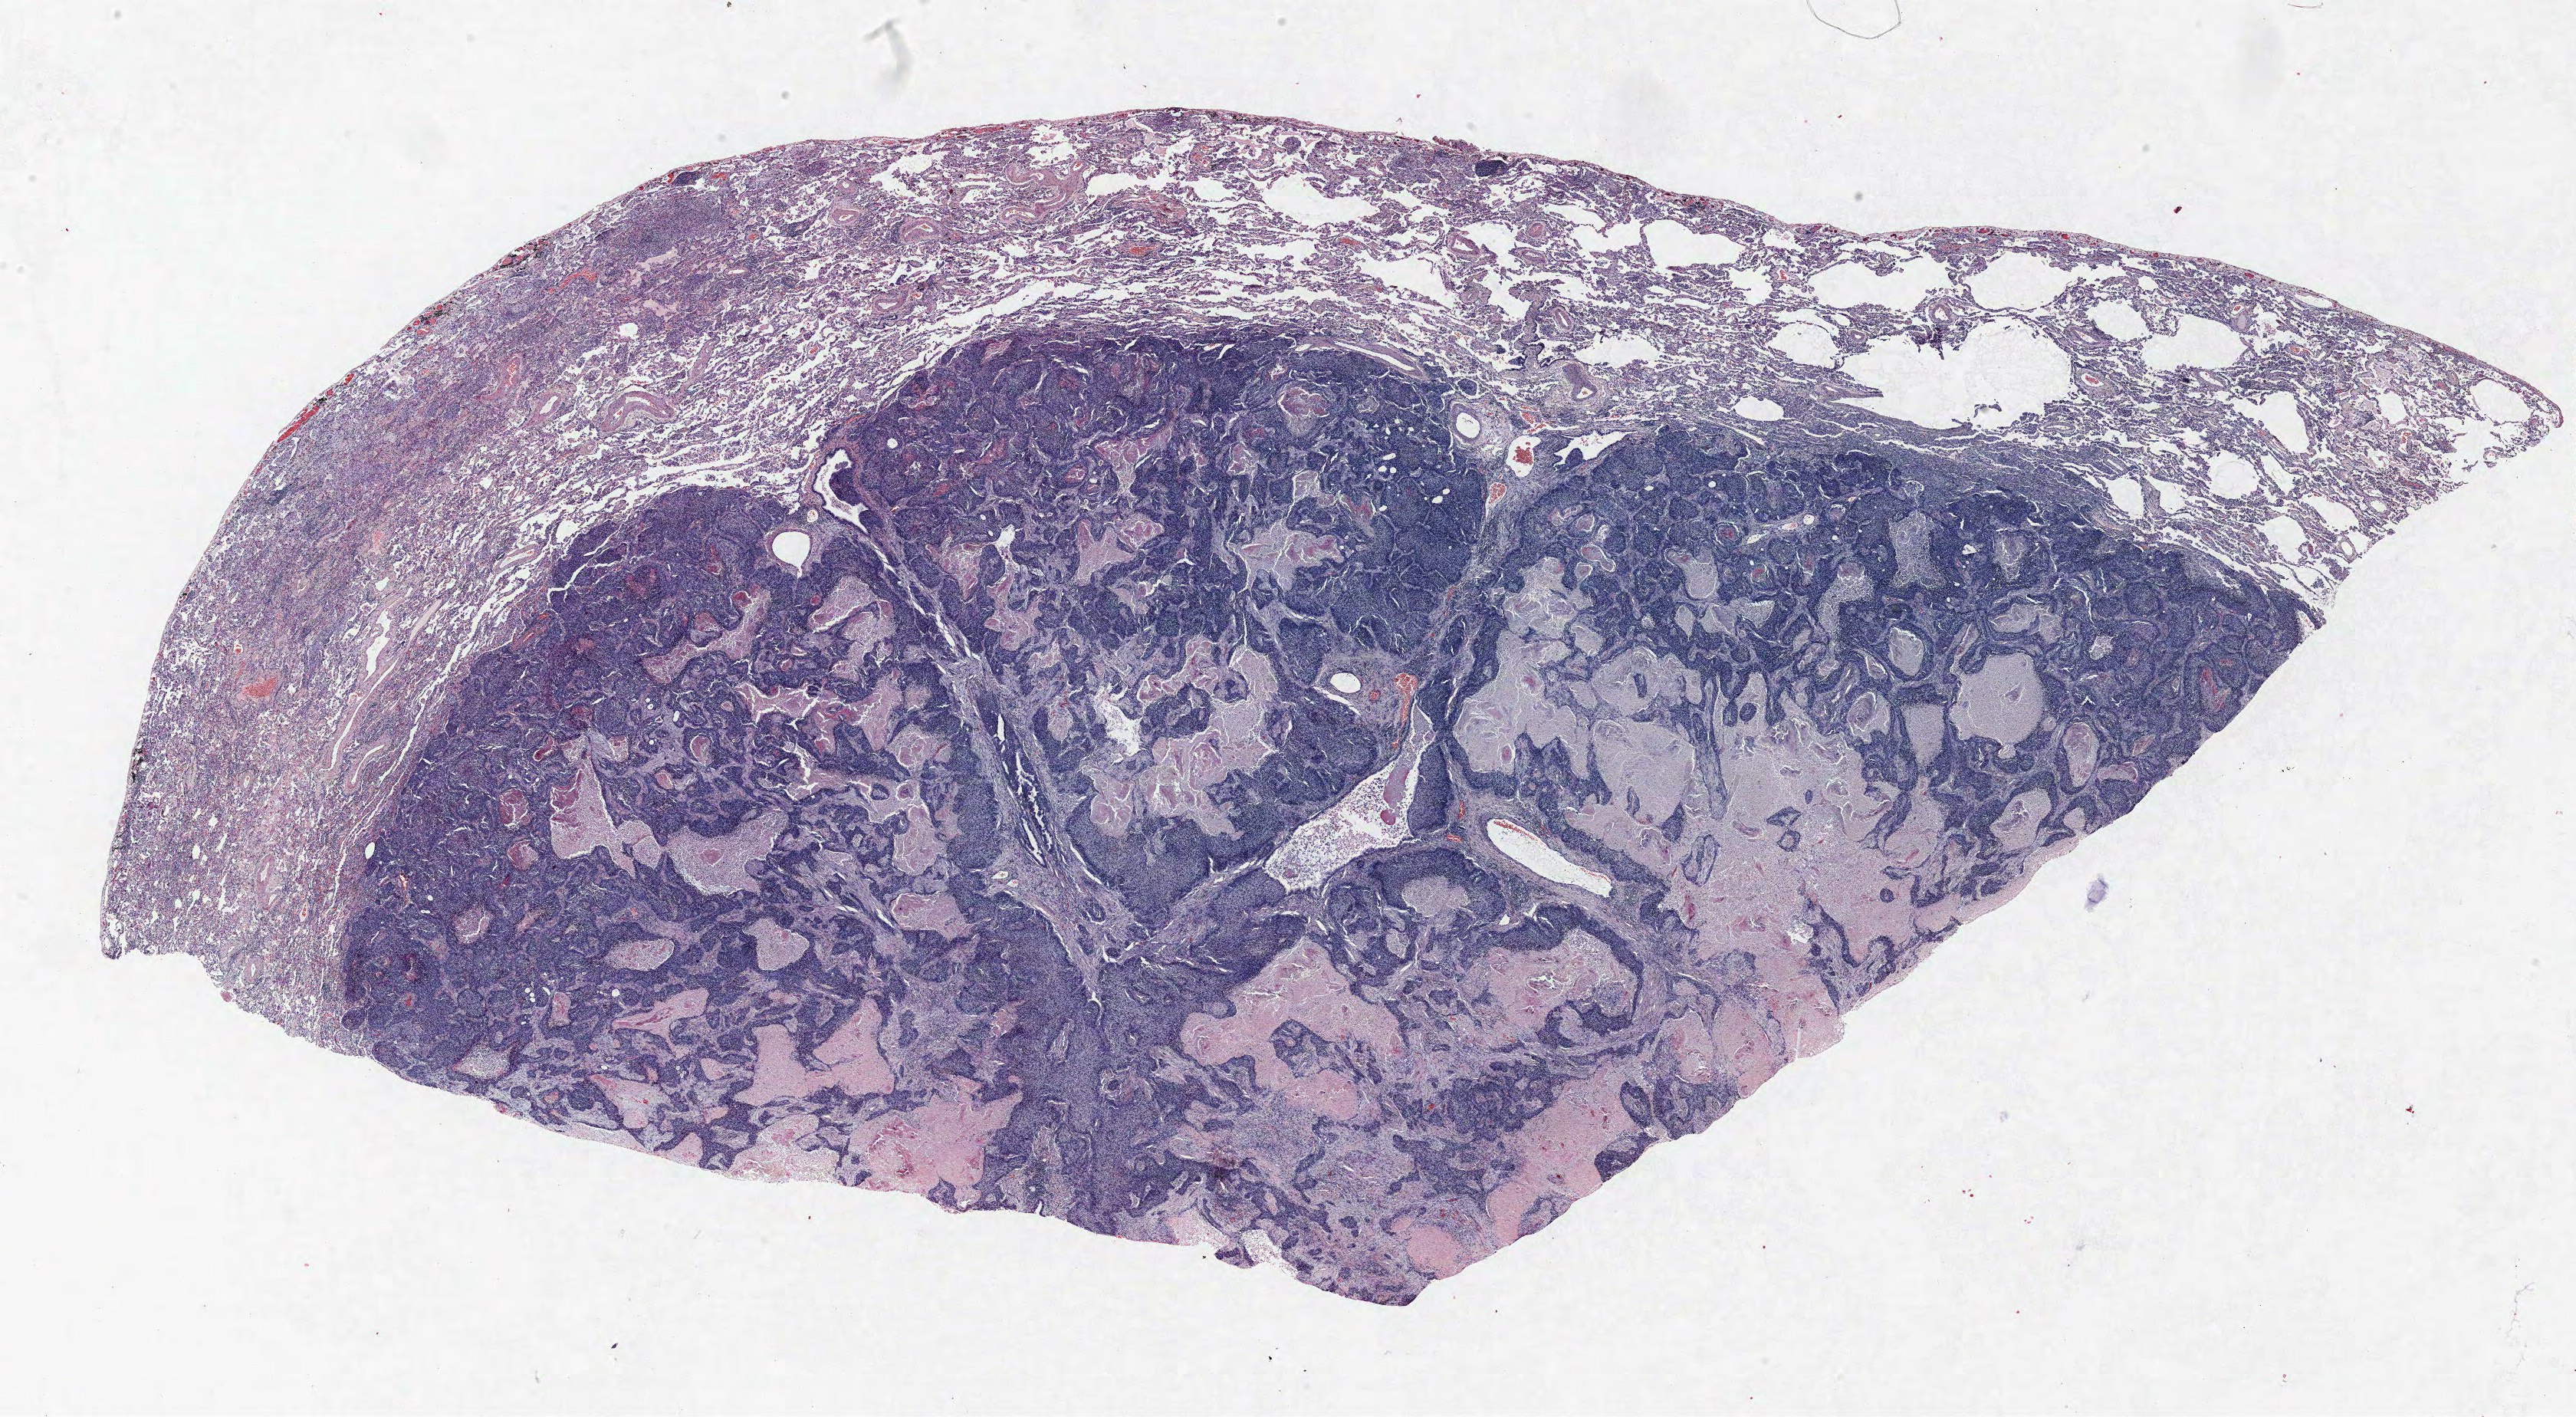
H&E whole-slide image — low-resolution overview of the scanned area, about 26.9 x 14.8 mm. FFPE section. Lung. Male patient, aged 62 at enrolment. Former smoker at enrolment. Grade: poorly differentiated (G3).
Stage (AJCC 6th edition): IB. Tumour size (pathology): 45 mm. Participant's lung-cancer diagnosis: Squamous cell carcinoma, NOS (ICD-O-3 8070/3). Primary tumour location (clinical record): right lower lobe.